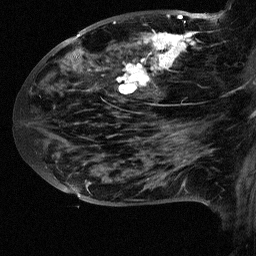
Breast MRI (dynamic contrast-enhanced), one sagittal slice. Position 31 of 64 along the scan axis. Dynamic contrast-enhanced study with each time point stored as its own series, time point 2 of 3 at this slice position (early post-contrast, ordered by acquisition time). 1.5 T. TE 4.5 ms, TR 11 ms. 256 × 256 image matrix, field of view 200 × 200 mm. Female patient, age 38 years. From the clinical record (not read from this slice): setting: breast cancer imaged before/during neoadjuvant chemotherapy; receptor status: HR-positive, HER2-negative.
Annotated regions visible in this slice (semi-automatically segmented with operator editing):
- analysis volume of interest (the breast-tissue region the enhancement analysis was run in; not a lesion): bounding box (x1, y1, x2, y2) in pixels: (88, 18, 252, 126)
- tumour enhancement mask (voxels above the 90 % enhancement threshold inside the analysis volume of interest): (116, 18, 251, 117)